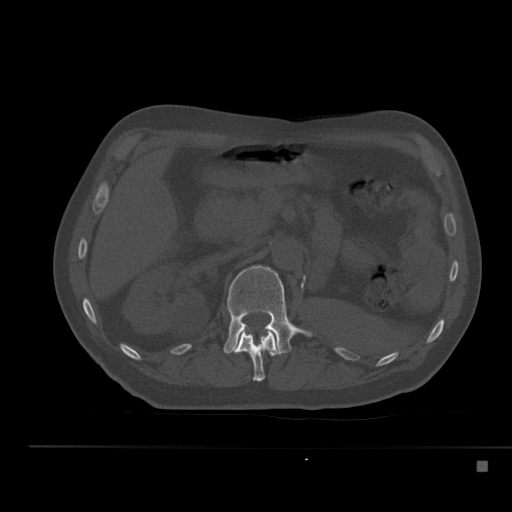
CT including the spine, one axial slice; slice 215 of 517 in the series (ordered by position); 120 kVp; bone window (W 1800 / L 400 HU); 1.5 mm slice thickness; 512 × 512 image matrix, field of view 408 × 408 mm. Male patient, age 70 years. From the clinical record (not read from this slice): primary cancer: renal.
Annotated regions visible in this slice (semi-automatically segmented with operator editing):
- L1 vertebra: bounding box [x1, y1, x2, y2] px = [223, 265, 312, 355]
- T12 vertebra: [232, 328, 279, 382]